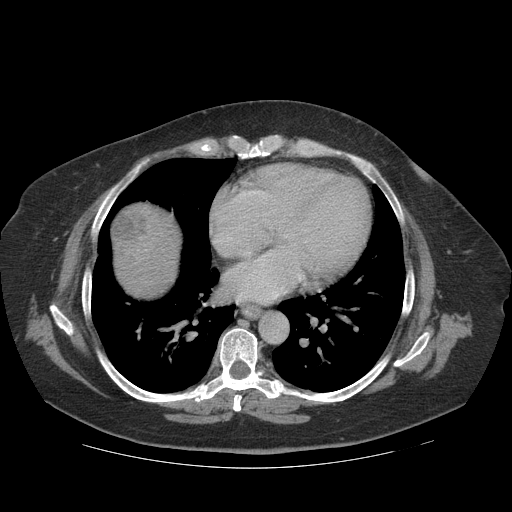
Contrast-enhanced abdominal CT (liver protocol), one axial slice; position 111 of 121 along the scan axis; reconstruction kernel STANDARD; 140 kVp; soft-tissue window (W 400 / L 40 HU); 2.5 mm slice thickness; 512 × 512 image matrix, field of view 420 × 420 mm. Case-level facts recorded for this patient, not image findings: diagnosis: hepatocellular carcinoma (patient treated with transarterial chemoembolisation; whether this scan precedes or follows treatment is not stated here); TNM stage (as recorded): Stage-IIIA; Child-Pugh class: A; tumour differentiation: well differentiated.
Structures marked on this image (semi-automatic segmentation, software-assisted and operator-edited):
- liver parenchyma outside the tumour (the mass and vessels are separate outlines, so this box may not span the whole liver): bounding box <112,202,180,296> (left, top, right, bottom; pixels)
- mass: <112,213,148,242>